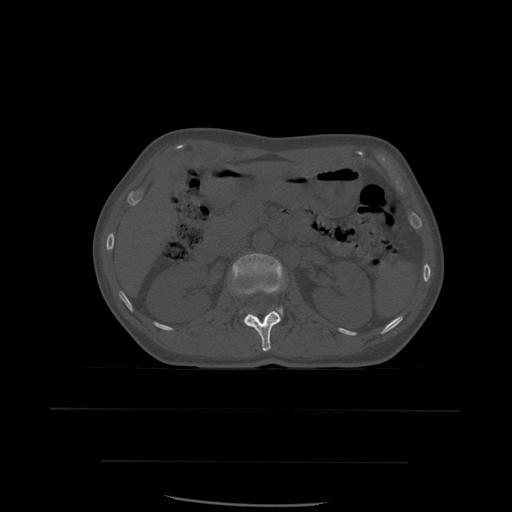
CT including the spine, one axial slice; slice 239 of 574 in the series (ordered by position); bone window (W 1800 / L 400 HU); 1.25 mm slice thickness; 512 × 512 image matrix, field of view 392 × 392 mm. Patient age 48 years. From the clinical record (not read from this slice): primary cancer: lung; vertebrae with lytic lesions (as recorded): T11.
Outlined on this slice (semi-automatically segmented with operator editing):
- L1 vertebra: box from (x=244, y=311) to (x=281, y=352) px
- L2 vertebra: (x=232, y=253)–(x=285, y=316)